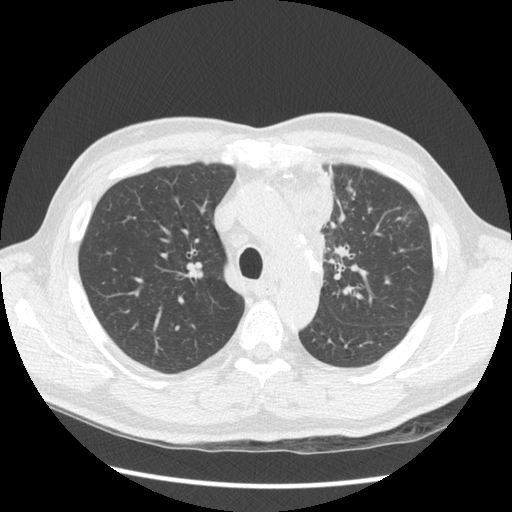
Low-dose screening chest CT, one axial slice. Position 100 of 136 along the scan axis. 120 kVp. Lung window (W 1500 / L -600 HU). 512 × 512 image matrix, field of view 360 × 360 mm.
Annotated regions visible in this slice (outlined manually by an expert reader):
- lesion 1 (tumor, upper lobe of left lung): bounding box [x1, y1, x2, y2] px = [299, 174, 333, 276]